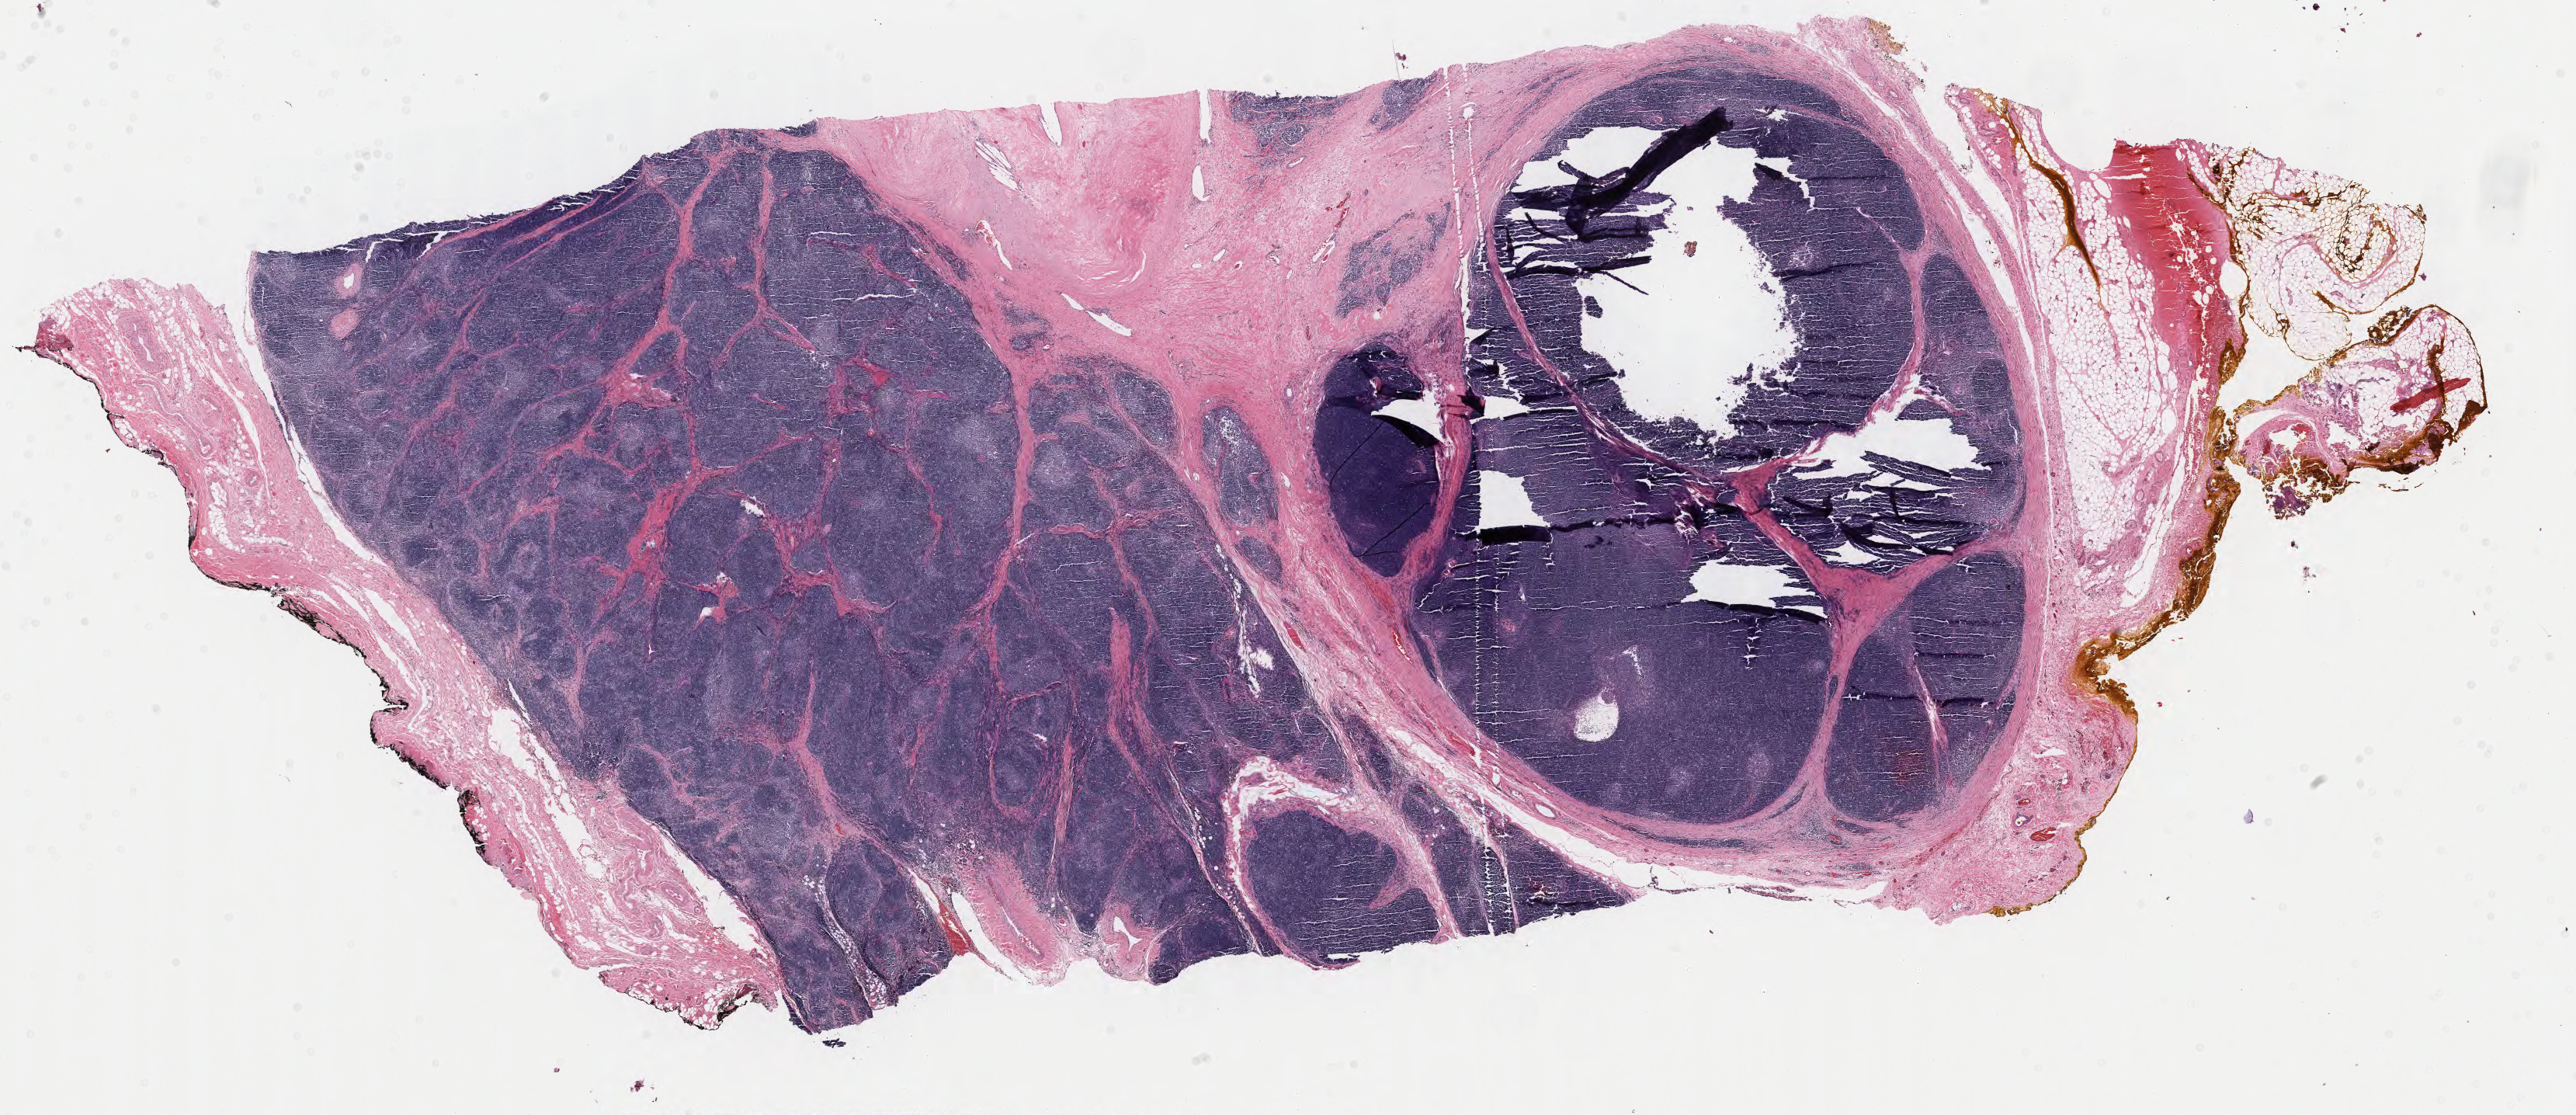
Whole-slide histology image, Hematoxylin and eosin (H&E) stained, a low-resolution overview of the entire scanned area, about 26.3 x 11.4 mm; FFPE section; sample: primary tumour, thymus. Patient: female, age at initial diagnosis 57 years.
Histologic diagnosis: Thymoma, type B1, NOS.